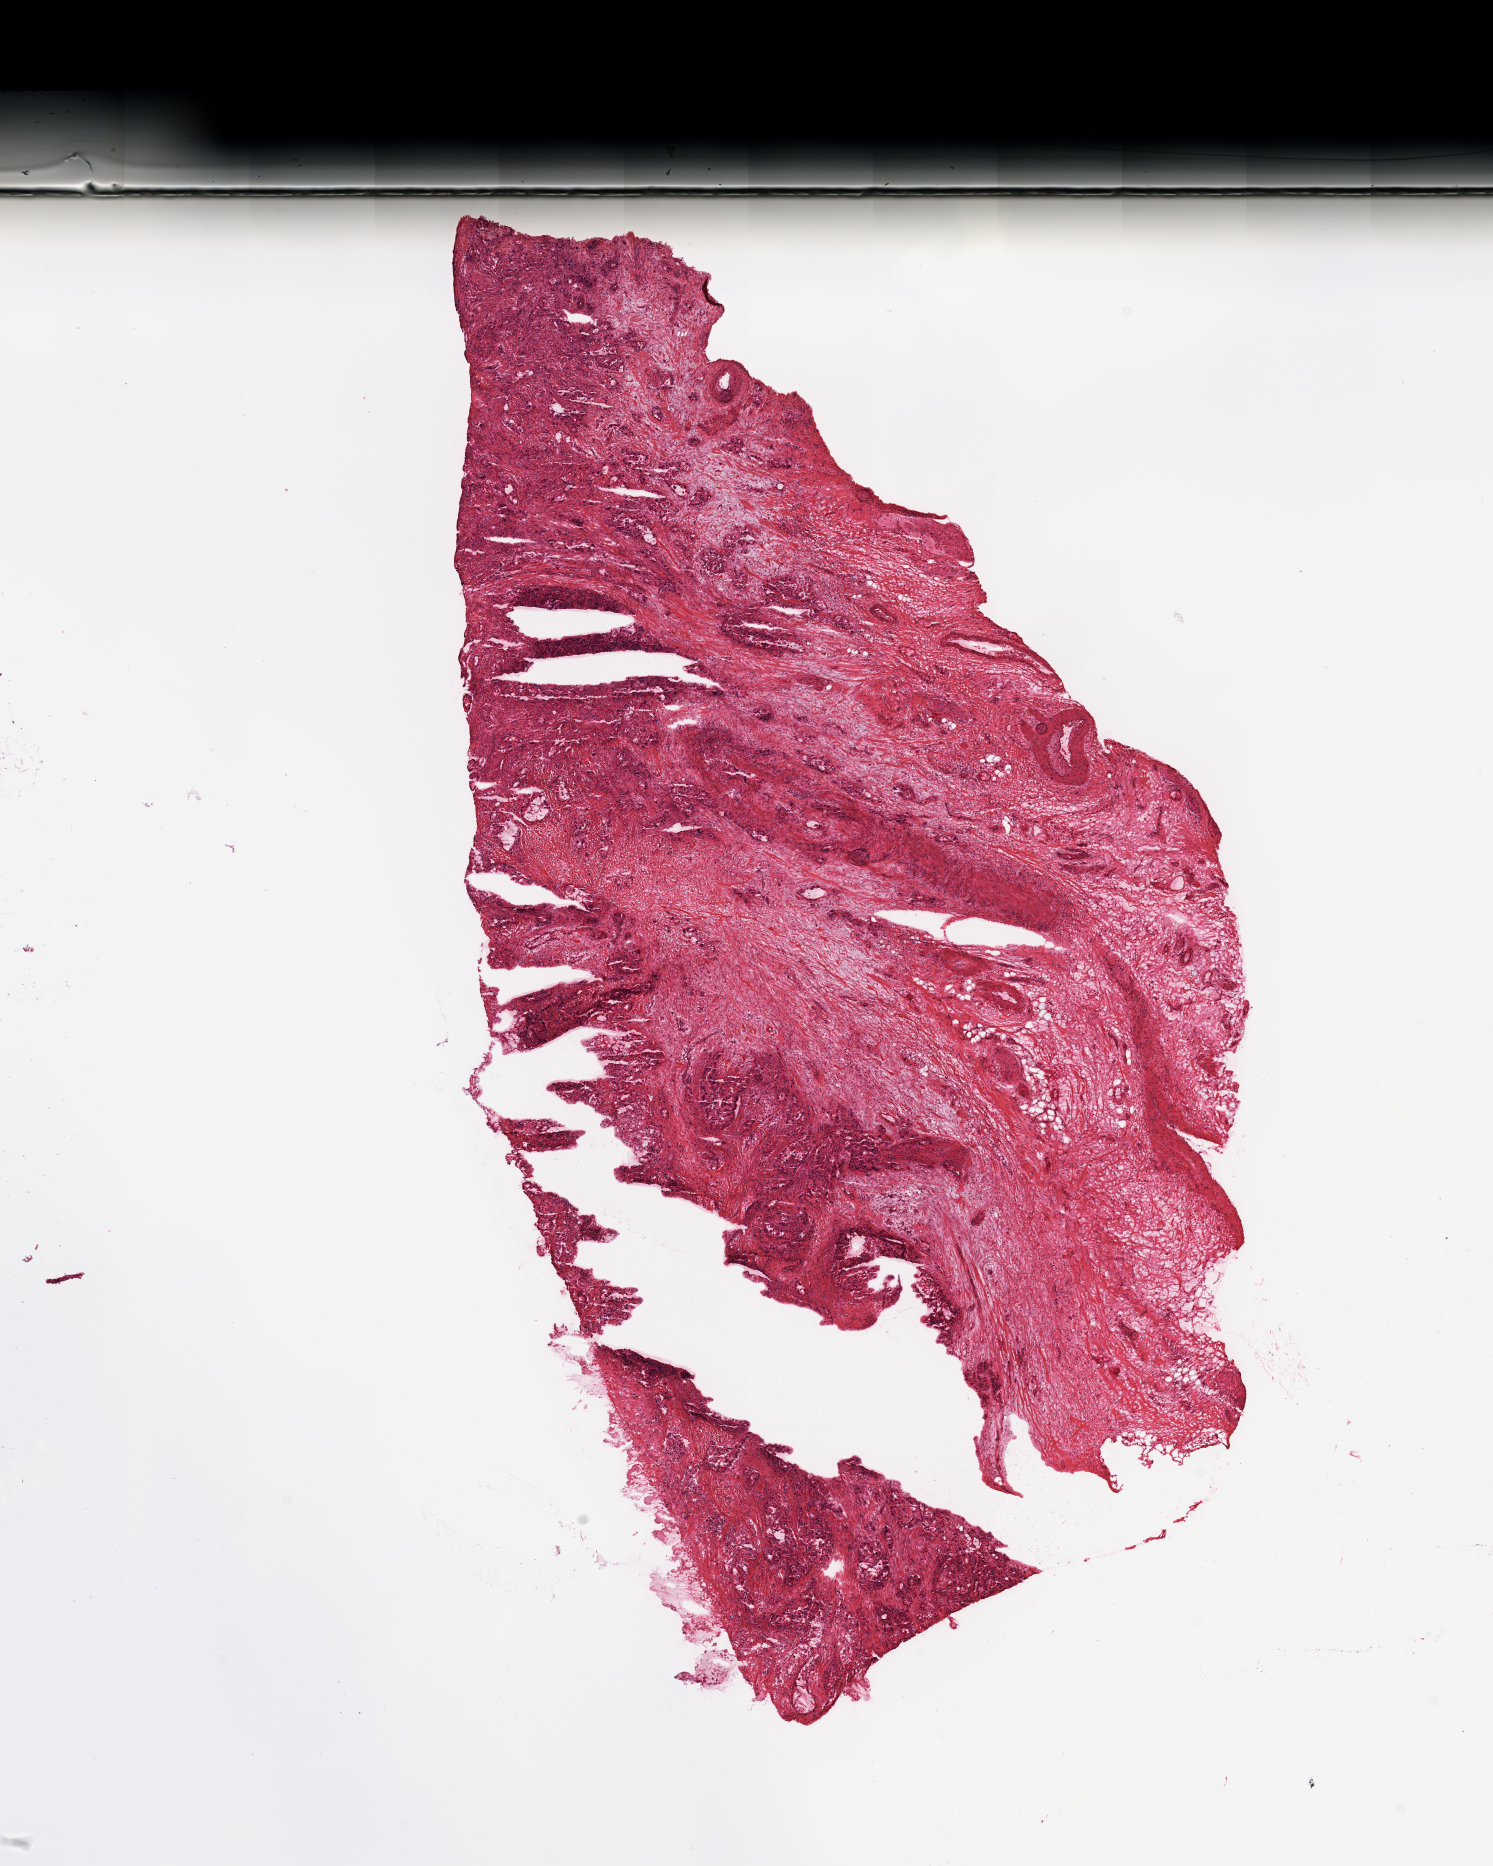
Whole-slide histology image, Hematoxylin and eosin (H&E) stained, a low-resolution overview of the entire scanned area, about 11.8 x 14.8 mm (acquisition: 20x scan); pancreas, tumour tissue. 61-year-old female patient. Histologic grade: G2 (moderately differentiated).
Histologic diagnosis: Infiltrating duct carcinoma, NOS. Primary tumour site (as recorded): head. AJCC pathologic stage: IIB.